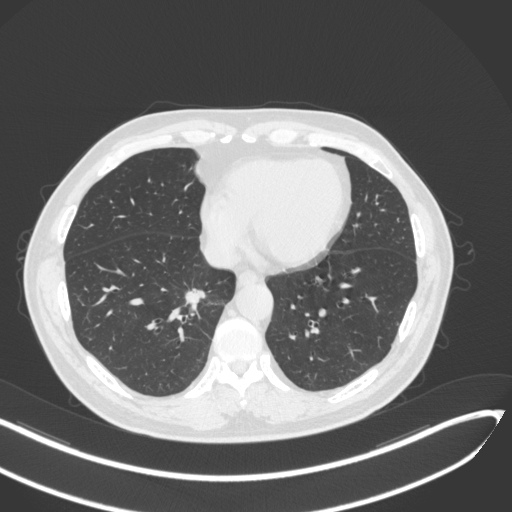
Chest CT, one axial slice; position 127 of 429 along the scan axis; reconstruction kernel B31f; 120 kVp; lung window (W 1500 / L -600 HU); 512 × 512 image matrix, field of view 400 × 400 mm. Patient: male, 62 years. Case-level facts recorded for this patient, not image findings: clinical TNM (as recorded): T1b N0 M0; histopathological grade: G2.
Annotated regions visible in this slice (rectangle marked by the reading radiologist):
- lung tumour (recorded histology: adenocarcinoma): bounding box (x1, y1, x2, y2) in pixels: (180, 286, 220, 321)